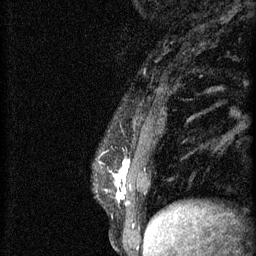
Breast MRI (dynamic contrast-enhanced), one sagittal slice. Position 16 of 60 along the scan axis. 3 images stored at this slice position (order not interpretable as contrast timing). 1.5 T. TE 4.2 ms, TR 11 ms. 2 mm slice thickness. 256 × 256 image matrix, field of view 180 × 180 mm. Patient: female, 37 years.
Structures marked on this image (semi-automatically segmented with operator editing):
- analysis volume of interest (the breast-tissue region the enhancement analysis was run in; not a lesion): bounding box (x1, y1, x2, y2) in pixels: (95, 160, 173, 221)
- tumour enhancement mask (voxels above the 70 % enhancement threshold inside the analysis volume of interest): (113, 160, 129, 201)